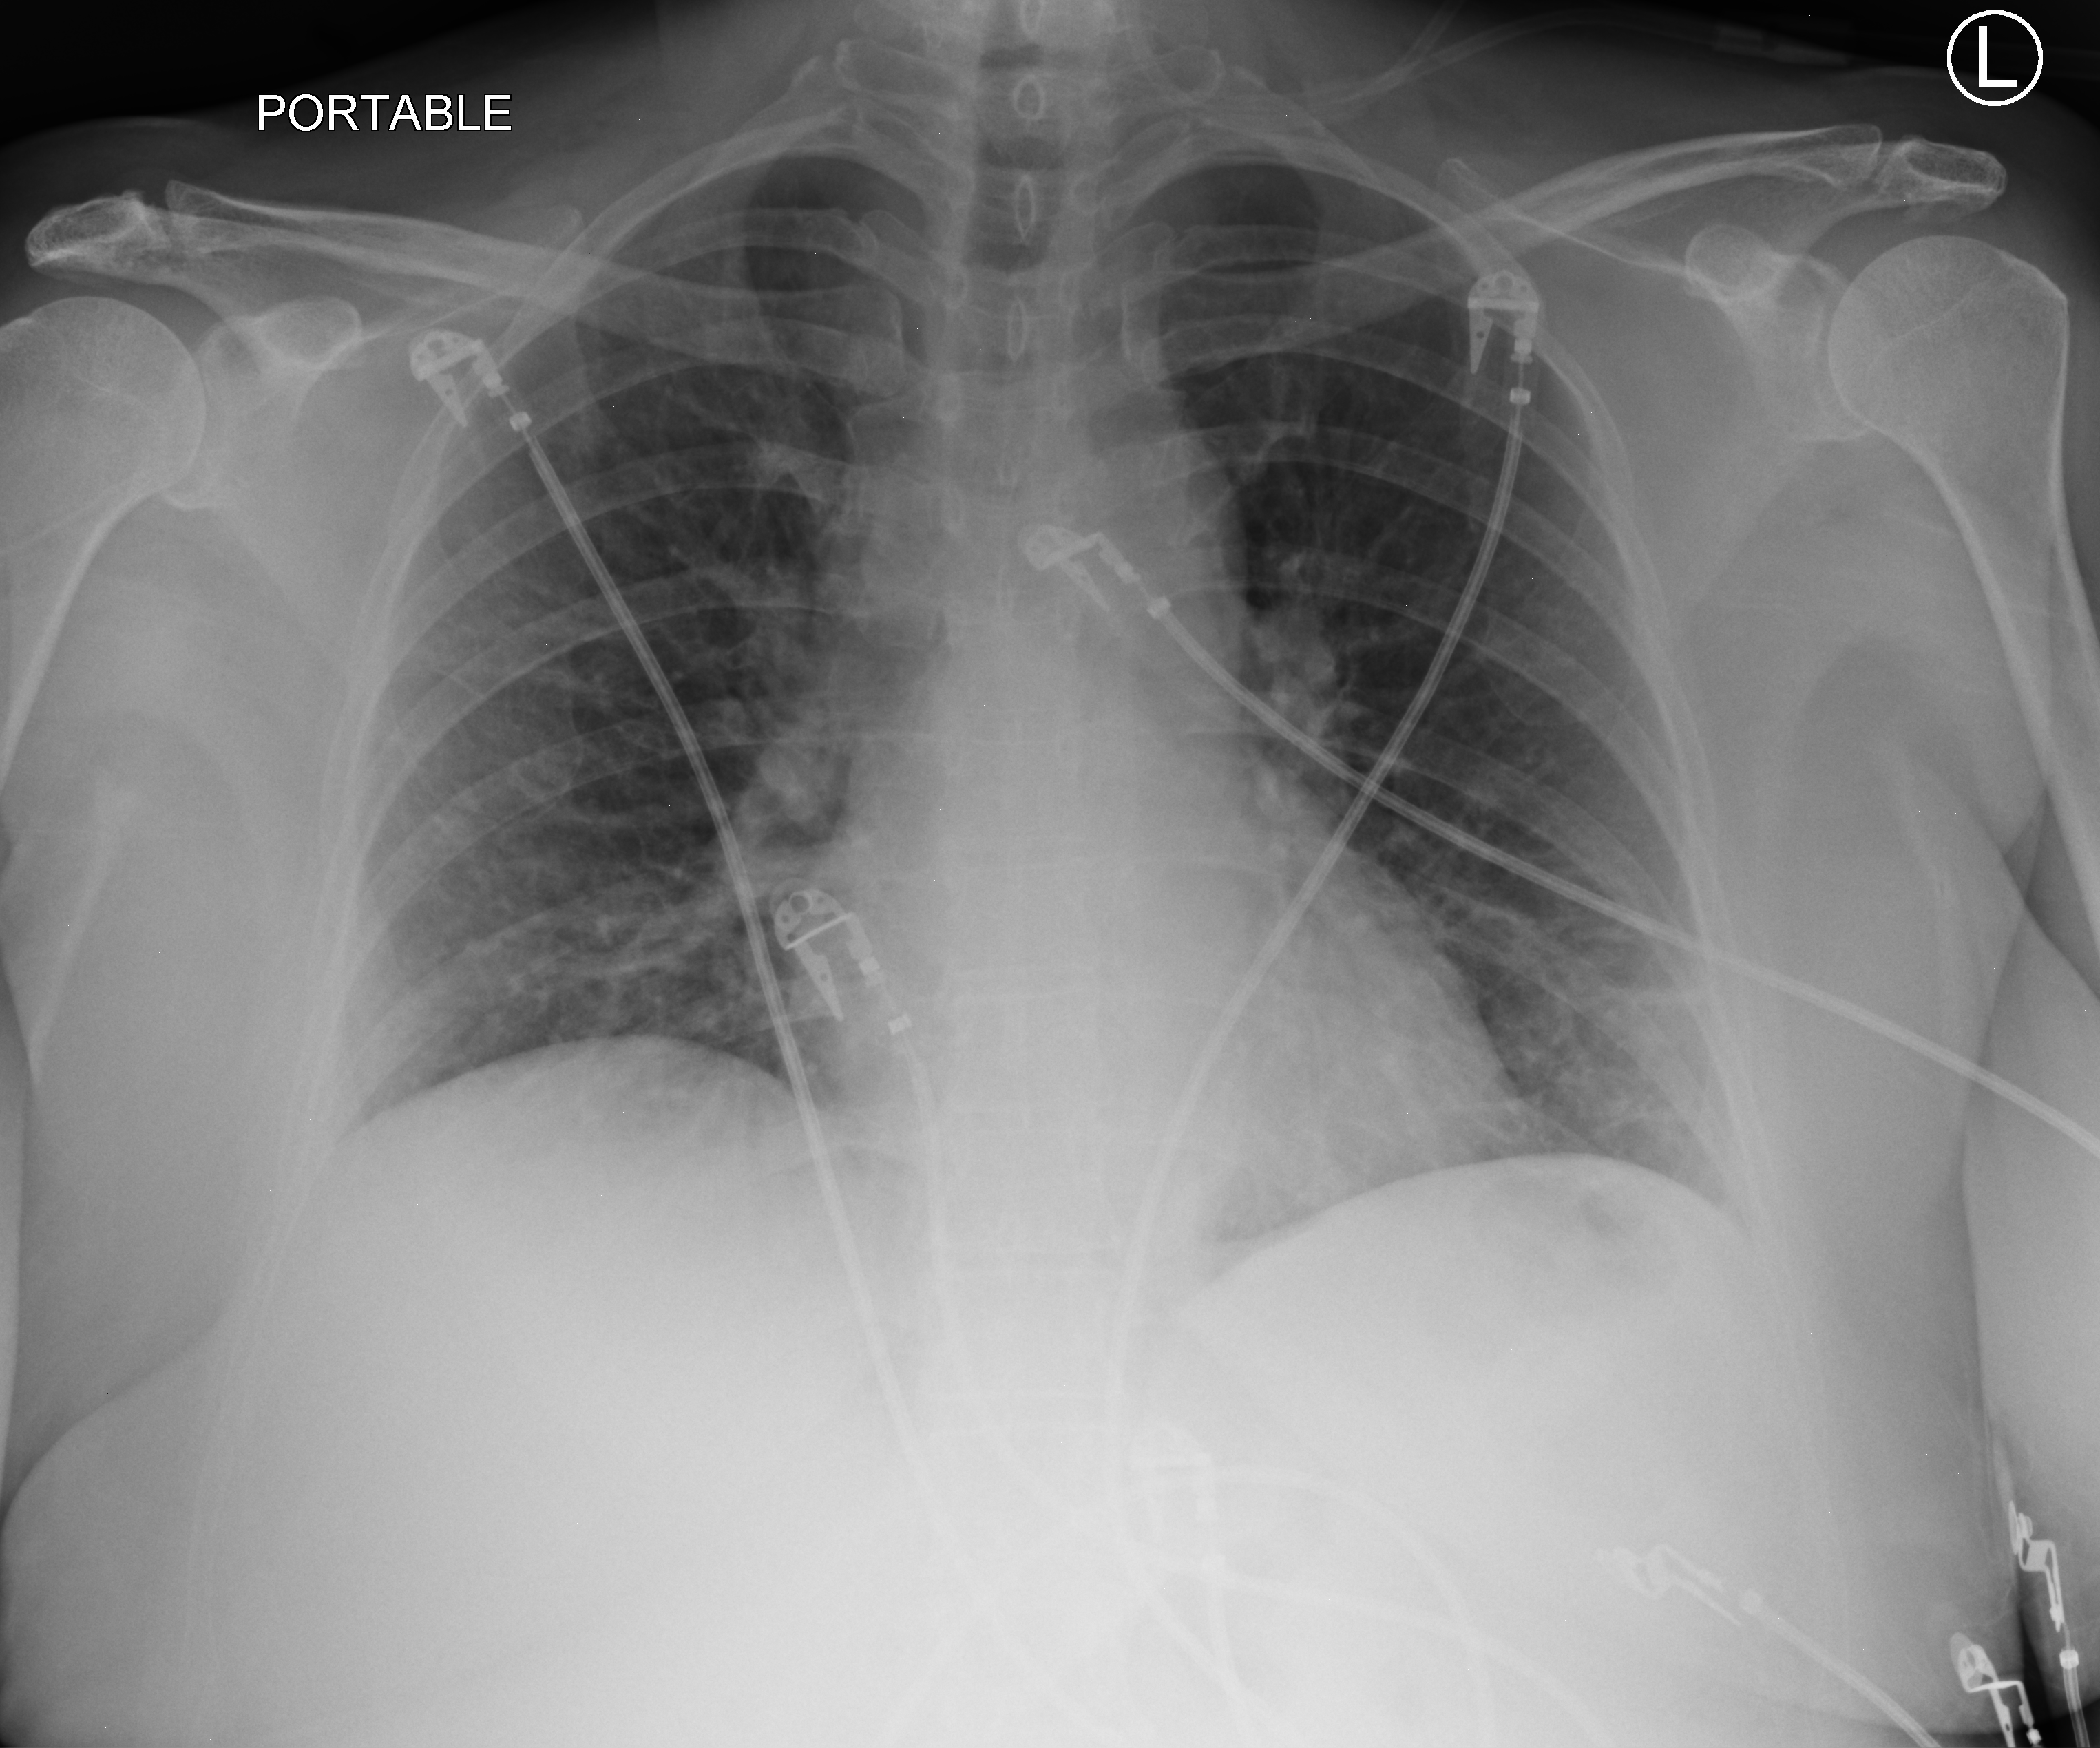
Bedside chest radiograph (computed radiography). Female patient hospitalised with COVID-19, age 60–74 years.
From the hospital-stay record, not from the radiograph (when in the stay this image was taken is not recorded): mechanically ventilated during this hospital stay: yes.